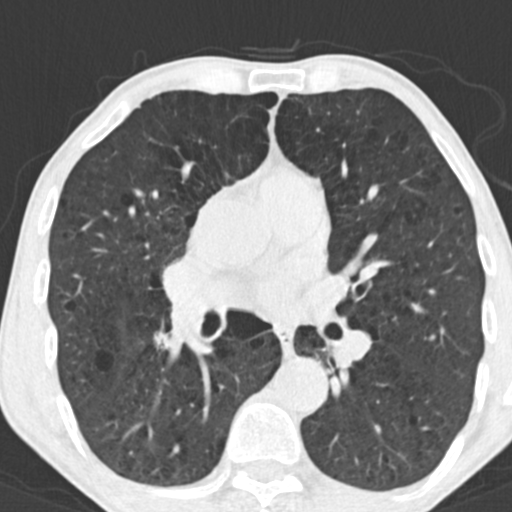
Axial slice from a low-dose chest CT screening exam, baseline screening round, lung window (W 1500 / L -600 HU), 2 mm slice thickness, standard (soft-tissue) reconstruction kernel (B30f). Male, age 64 years at enrolment.
- Lesion marked by an expert reader, bounding box <137,318,190,364> (left, top, right, bottom; pixels).
- No non-calcified nodule or mass ≥4 mm was recorded by the screening reader at this exam.
- Official screen result: negative screen, significant abnormalities not suspicious for lung cancer.